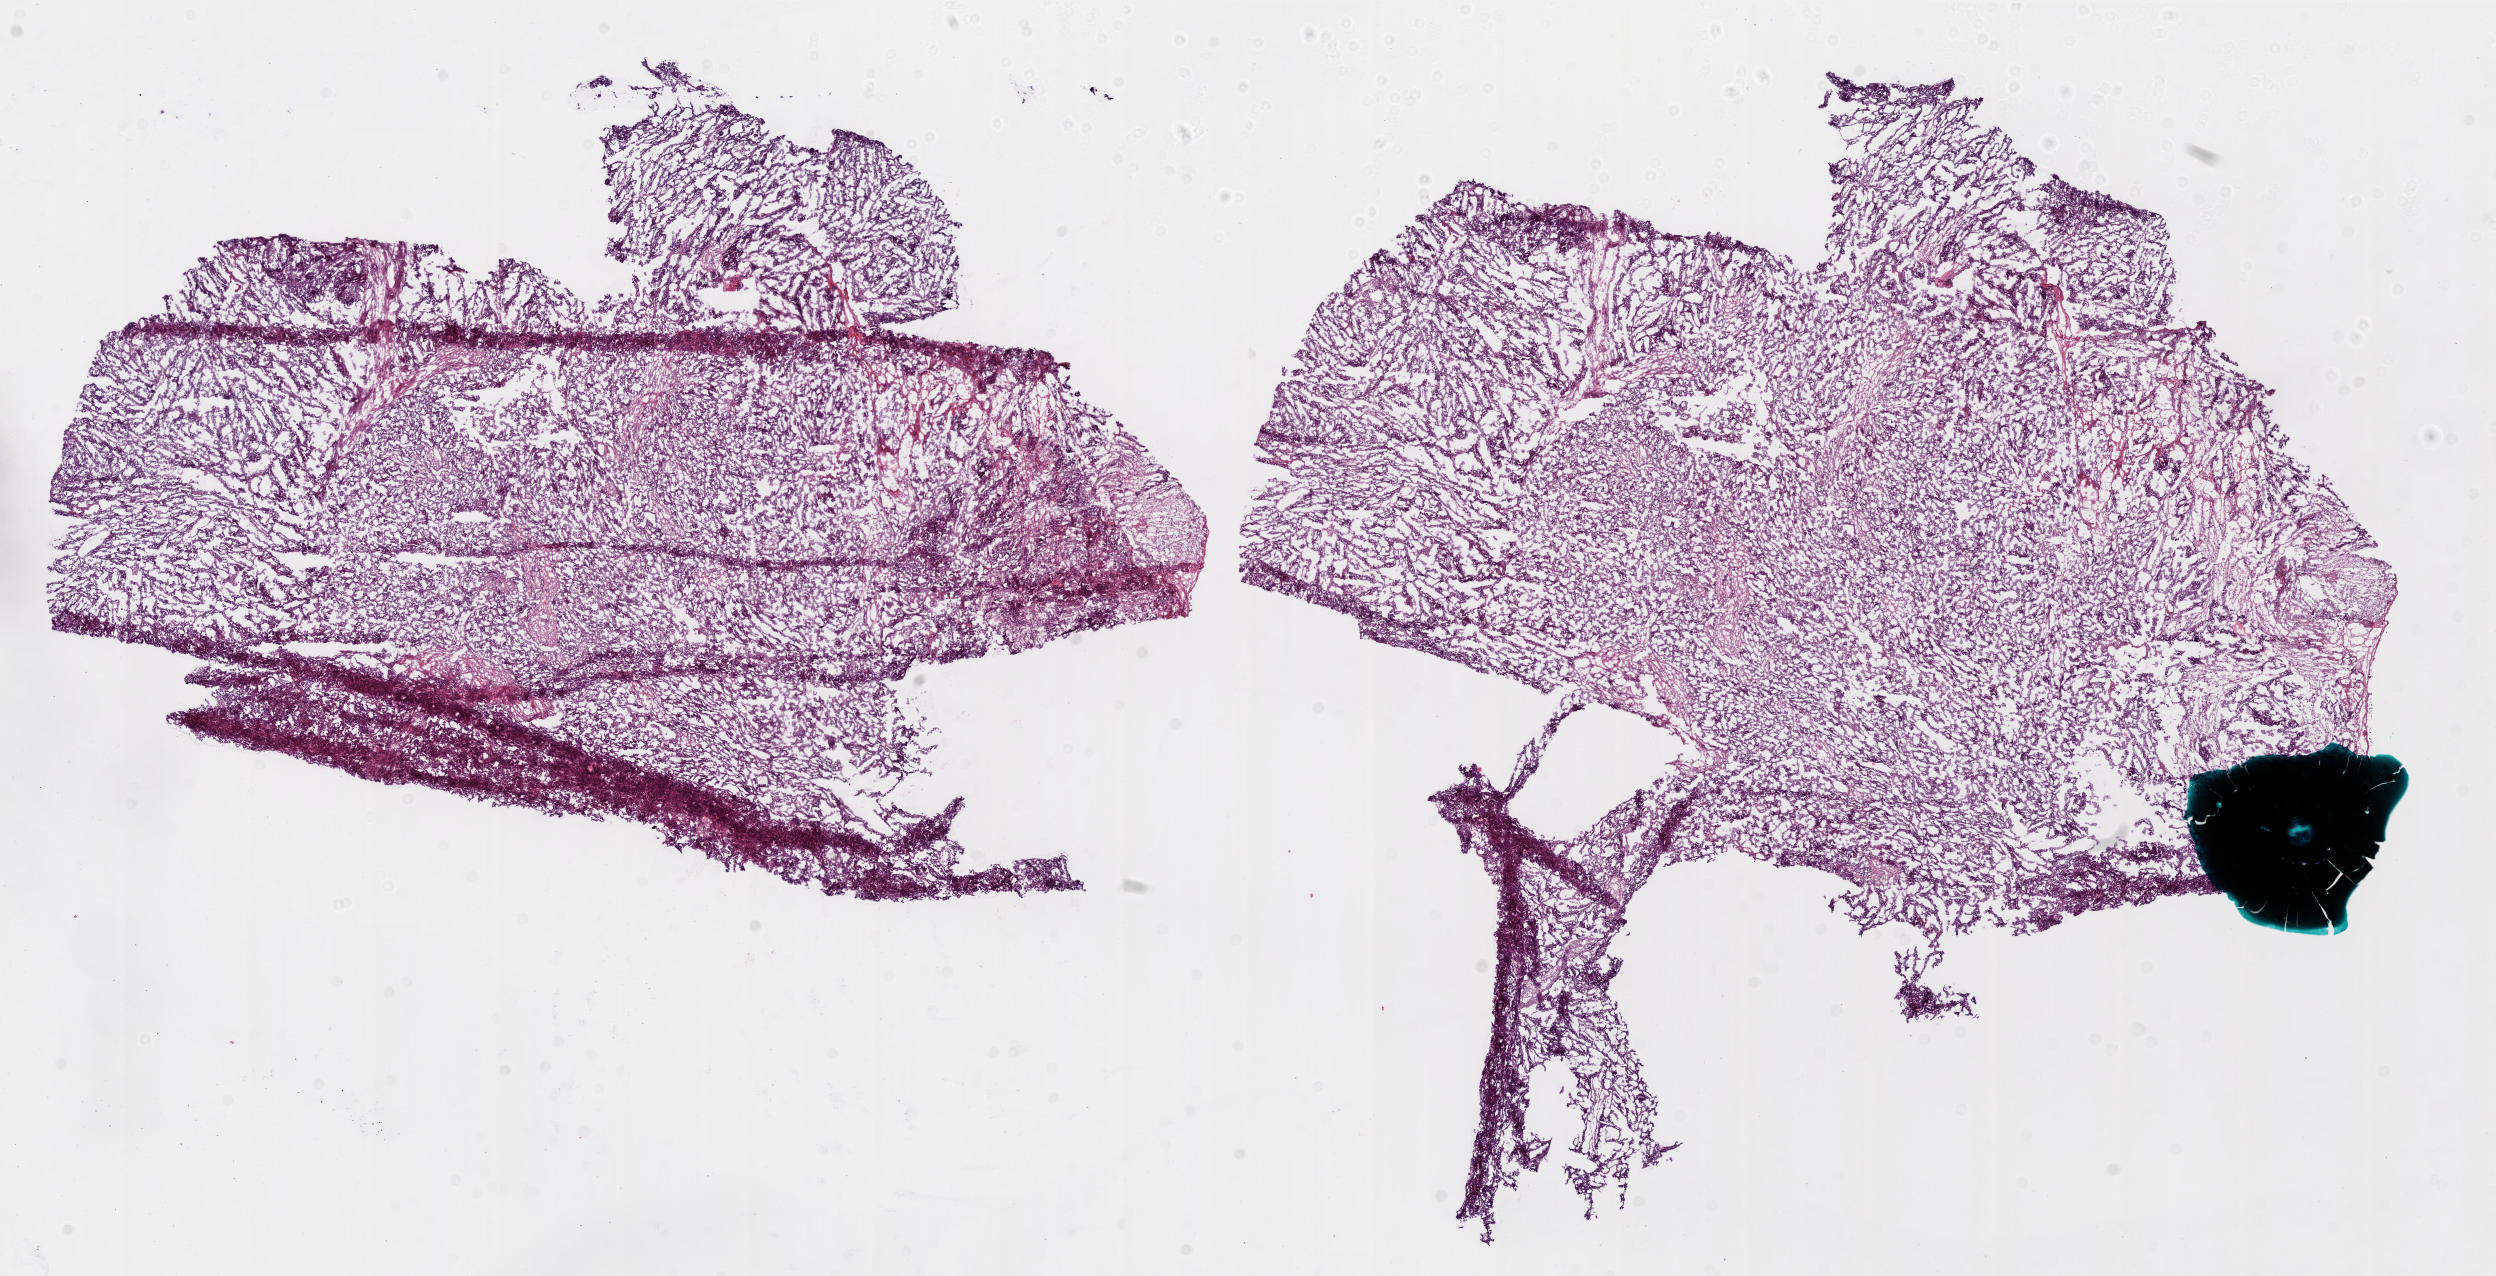
Whole-slide histology image, Hematoxylin and eosin (H&E) stained — shown as a low-resolution overview of the whole scanned area (about 20.0 x 10.2 mm, from a 20x scan), frozen section from the bottom of the tissue portion, ovary, primary tumour sample. Female, age 62 years at initial diagnosis. Histologic grade: G3 (poorly differentiated). Pathologist review of this section (percent, as recorded): tumour cells 0%, tumour nuclei 95%, normal cells 0%, stromal cells 0%, necrosis 5%.
FIGO stage: IIIC. Pathologic diagnosis: Serous cystadenocarcinoma, NOS.